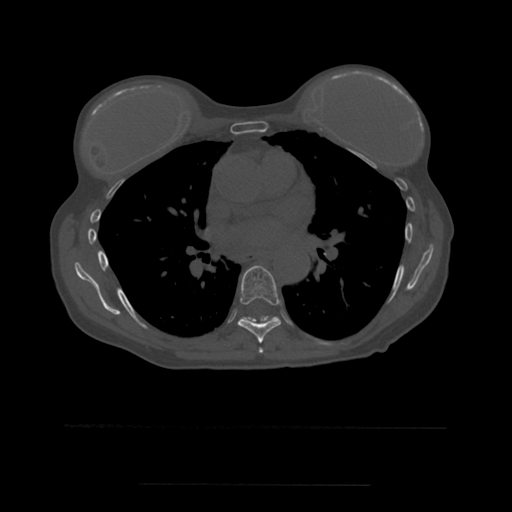
CT including the spine, one axial slice. Slice 355 of 544 in the series (ordered by position). Bone window (W 1800 / L 400 HU). 1.25 mm slice thickness. 512 × 512 image matrix. Patient age 58 years. Case-level facts recorded for this patient, not image findings: primary cancer: lung.
Annotated regions visible in this slice (semi-automatic segmentation, software-assisted and operator-edited):
- T6 vertebra: bounding box <259,348,264,354> (left, top, right, bottom; pixels)
- T7 vertebra: <238,266,282,343>
- T8 vertebra: <244,317,273,323>